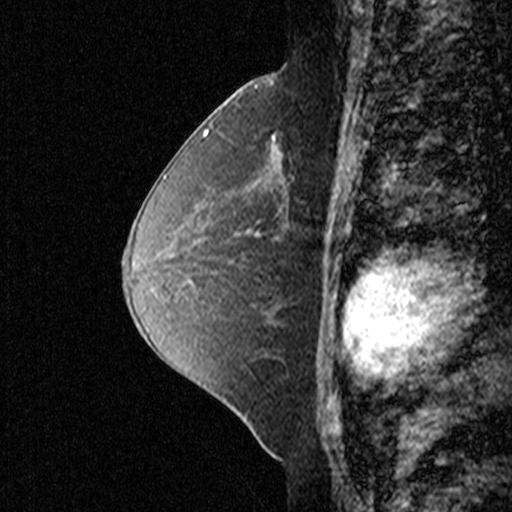
Breast MRI (dynamic contrast-enhanced), one sagittal slice. Slice 22 of 44 in the series (ordered by position). Dynamic contrast-enhanced study with each time point stored as its own series, time point 2 of 3 at this slice position (early post-contrast, ordered by acquisition time). 1.5 T. TE 4.5 ms, TR 11 ms. 3 mm slice thickness. 512 × 512 image matrix, field of view 200 × 200 mm. Female patient, age 49 years. From the clinical record (not read from this slice): setting: breast cancer imaged before/during neoadjuvant chemotherapy; receptor status: triple-negative.
Annotated regions visible in this slice (semi-automatic segmentation, software-assisted and operator-edited):
- analysis volume of interest (the breast-tissue region the enhancement analysis was run in; not a lesion): box from (x=236, y=100) to (x=335, y=197) px
- tumour enhancement mask (voxels above the 90 % enhancement threshold inside the analysis volume of interest): (x=272, y=133)–(x=293, y=186)